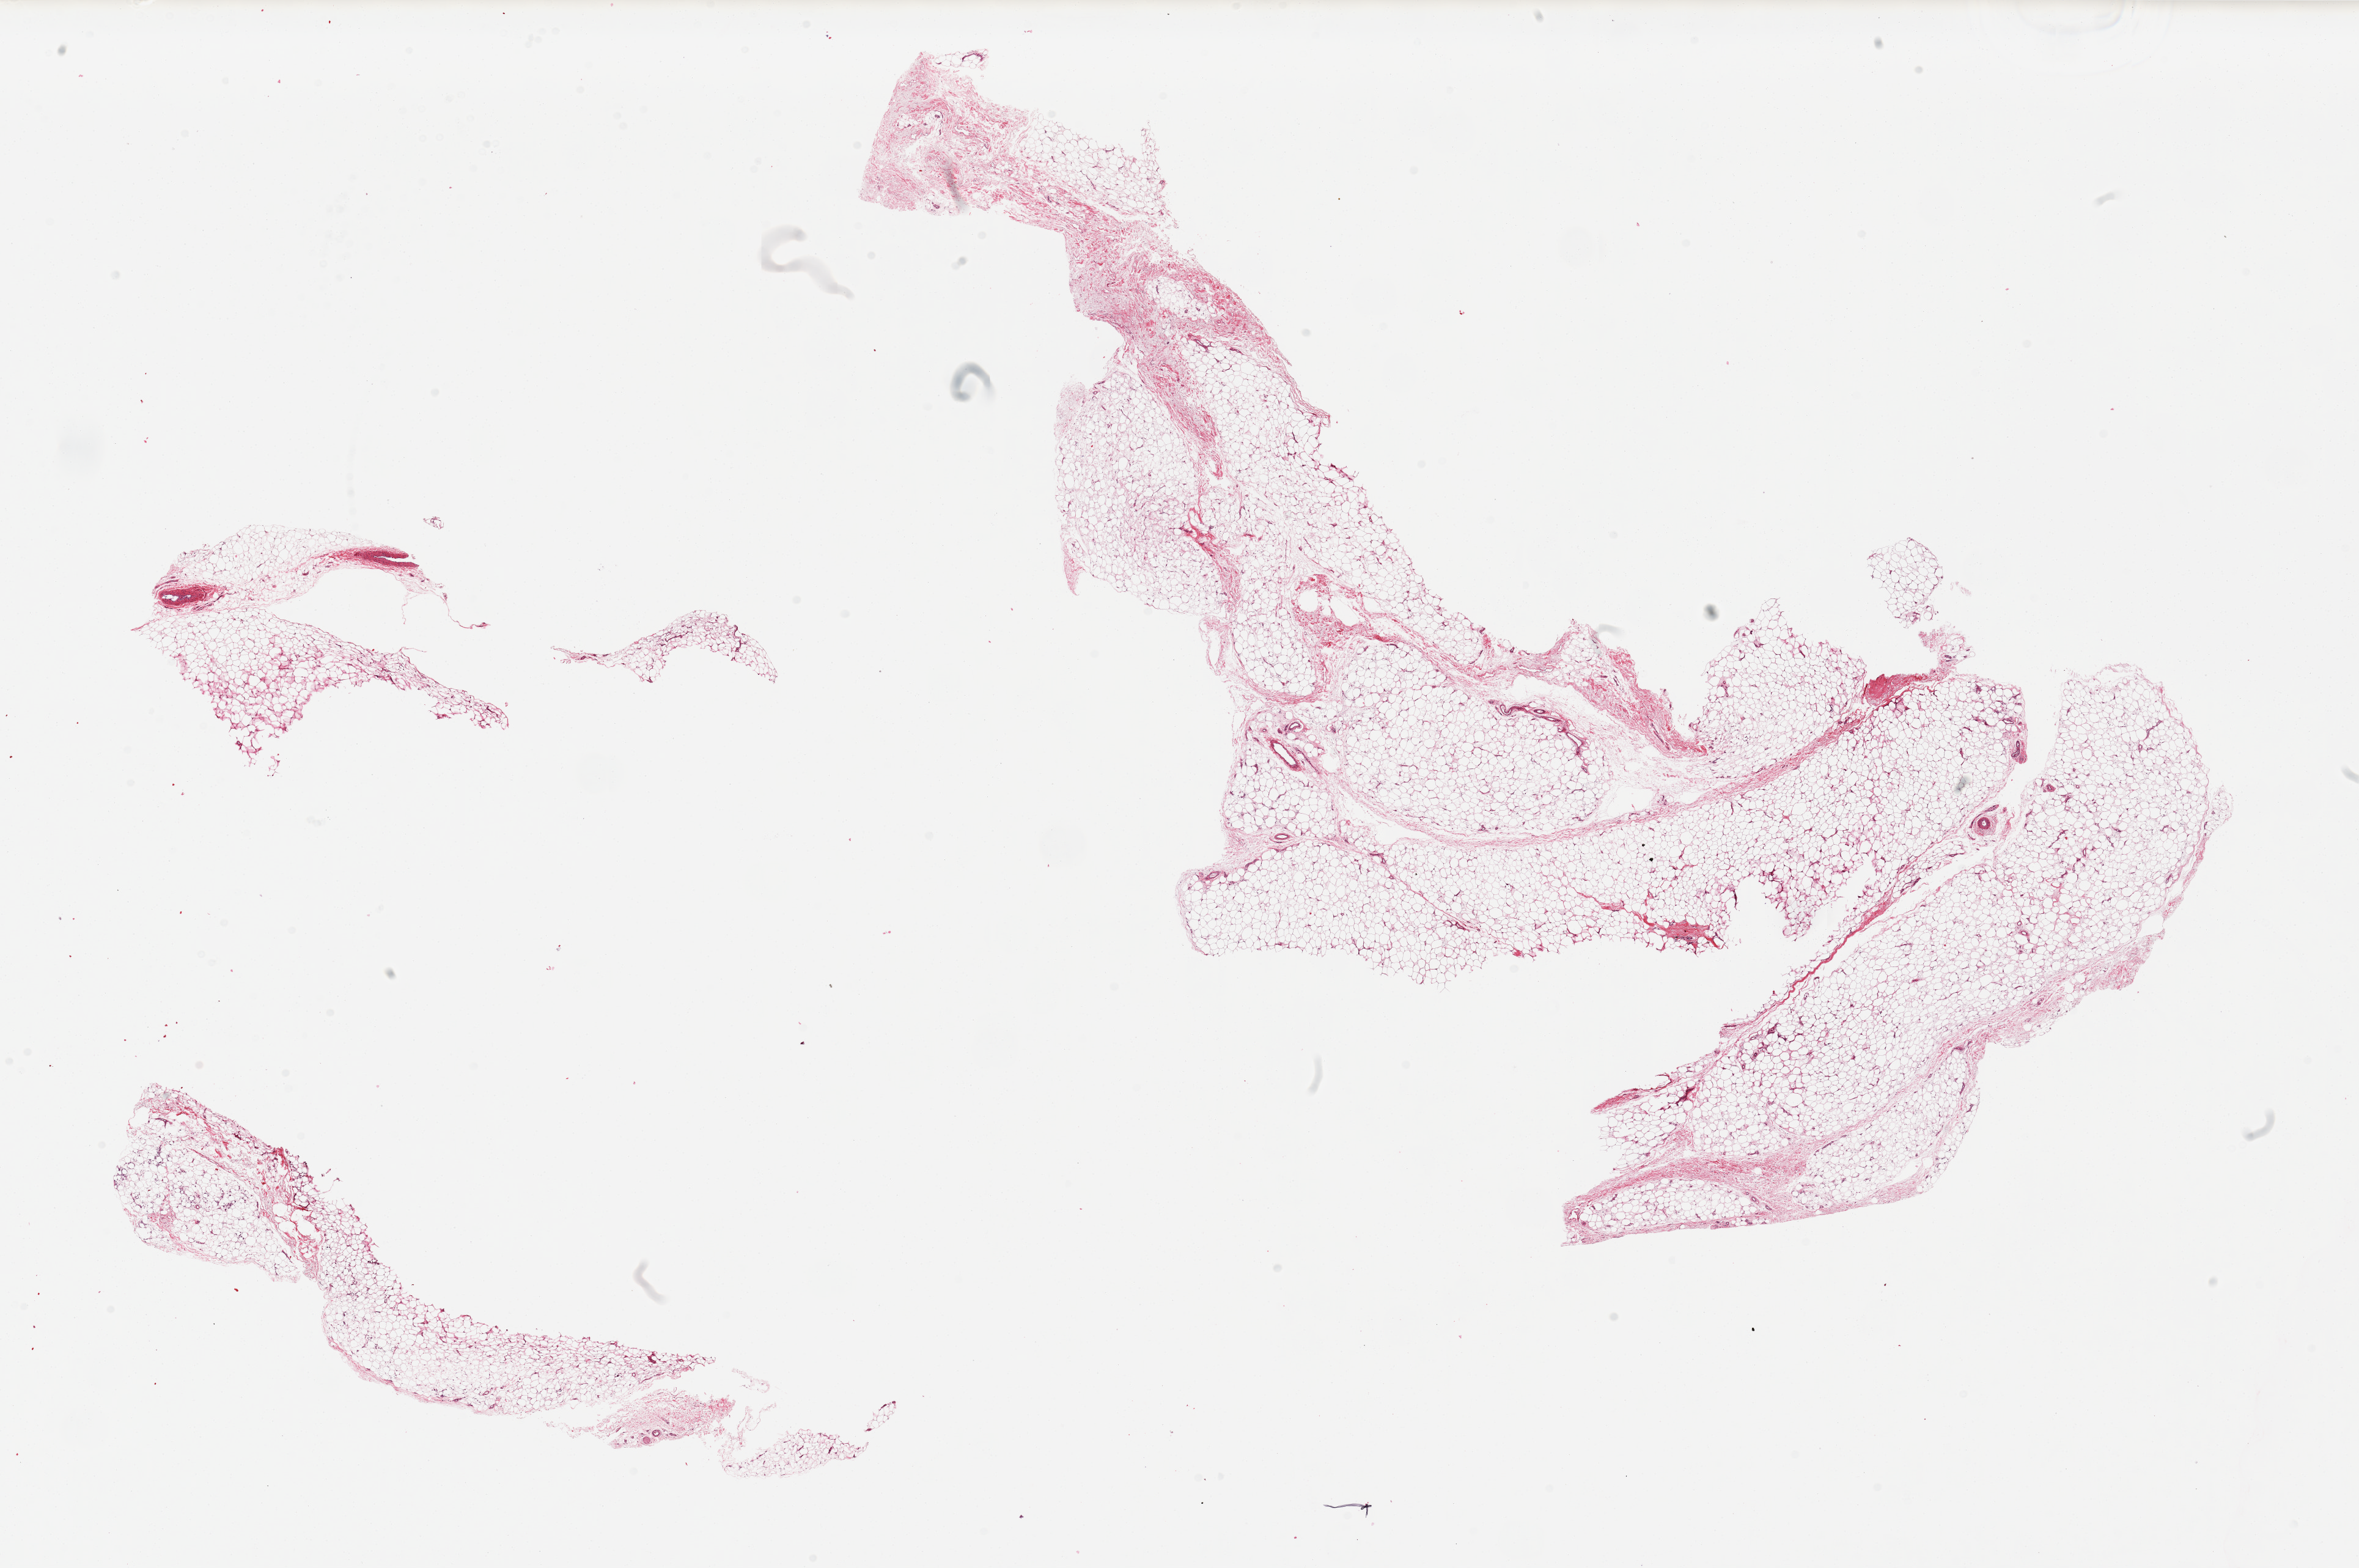
Digitized haematoxylin and eosin-stained section — low-resolution overview of the scanned area, about 30.5 x 20.3 mm (acquisition: 20x scan), PAXgene-fixed paraffin-embedded (PFPE) section, target tissue: adipose tissue, donor tissue sample. Donor: male.
• pathologist's review note for this sample: 2 pieces; incomplete sections (?poor fixation), tissue present is oversized at 20mm